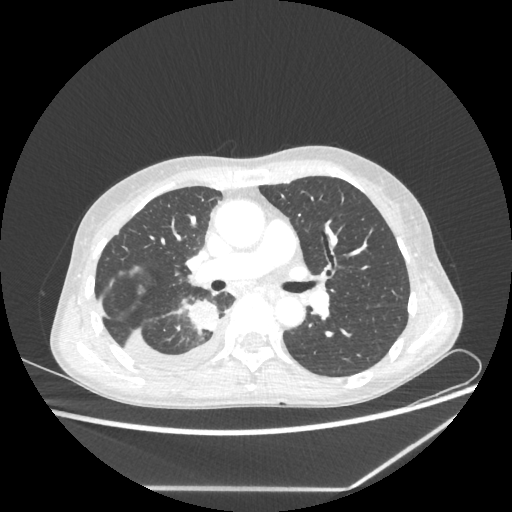
Chest CT, one axial slice; position 134 of 237 along the scan axis; reconstruction kernel STANDARD; 80 kVp; lung window (W 1500 / L -600 HU); 1.25 mm slice thickness; 512 × 512 image matrix, field of view 364 × 364 mm. Female patient, age 59 years. From the clinical record (not read from this slice): clinical TNM (as recorded): T1c N1 M1.
Outlined on this slice (bounding box drawn by a radiologist):
- lung tumour (recorded histology: adenocarcinoma): bounding box [x1, y1, x2, y2] px = [184, 299, 221, 334]